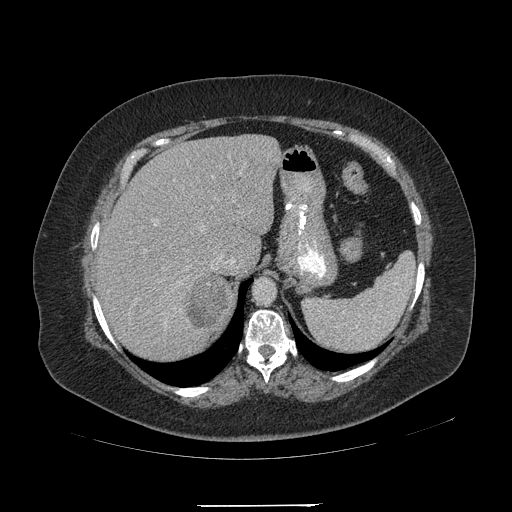
Contrast-enhanced abdominal CT, one axial slice; position 162 of 217 along the scan axis; intravenous contrast given; soft-tissue window (W 400 / L 40 HU); 512 × 512 image matrix, field of view 453 × 453 mm. Female patient, age 55 years. From the clinical record (not read from this slice): diagnosis: adrenocortical carcinoma; tumour side: right adrenal; tumour size at pathology: 11 cm; Ki-67 index: 20 %; stage (as recorded): 2.
Outlined on this slice (semi-automatic segmentation, software-assisted and operator-edited):
- mass: box from (x=186, y=276) to (x=226, y=328) px